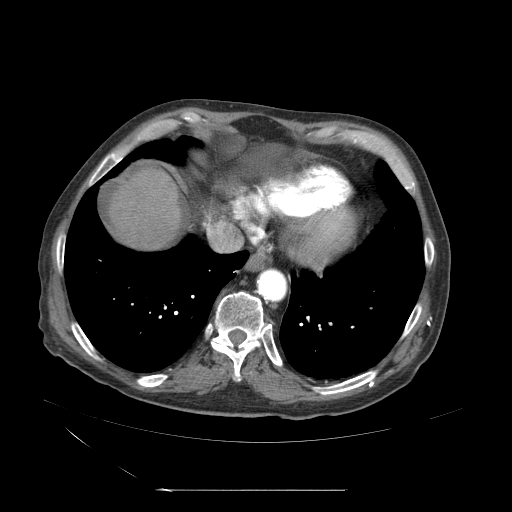
Contrast-enhanced abdominal CT (liver protocol), one axial slice. Slice 56 of 71 in the series (ordered by position). Reconstruction kernel STANDARD. Soft-tissue window (W 400 / L 40 HU). 512 × 512 image matrix, field of view 440 × 440 mm. Case-level facts recorded for this patient, not image findings: diagnosis: hepatocellular carcinoma (patient treated with transarterial chemoembolisation; whether this scan precedes or follows treatment is not stated here); TNM stage (as recorded): Stage-II; Child-Pugh class: A; tumour nodularity: multinodular; tumour size: 1 cm.
Structures marked on this image (semi-automatic segmentation, software-assisted and operator-edited):
- abdominal aorta: box from (x=258, y=268) to (x=288, y=303) px
- liver parenchyma outside the tumour (the mass and vessels are separate outlines, so this box may not span the whole liver): (x=117, y=165)–(x=205, y=255)